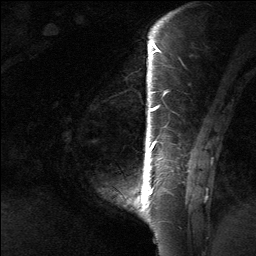
Breast MRI (dynamic contrast-enhanced), one sagittal slice; slice 14 of 64 in the series (ordered by position); dynamic contrast-enhanced study with each time point stored as its own series, time point 2 of 3 at this slice position (early post-contrast, ordered by acquisition time); 1.5 T; TE 4.8 ms, TR 27 ms; 2 mm slice thickness; 256 × 256 image matrix, field of view 180 × 180 mm. Female patient, age 39 years. From the clinical record (not read from this slice): setting: breast cancer imaged before/during neoadjuvant chemotherapy; receptor status: HER2-positive.
Annotated regions visible in this slice (semi-automatic segmentation, software-assisted and operator-edited):
- analysis volume of interest (the breast-tissue region the enhancement analysis was run in; not a lesion): bounding box [x1, y1, x2, y2] px = [105, 40, 201, 217]
- tumour enhancement mask (voxels above the 90 % enhancement threshold inside the analysis volume of interest): [136, 43, 159, 202]